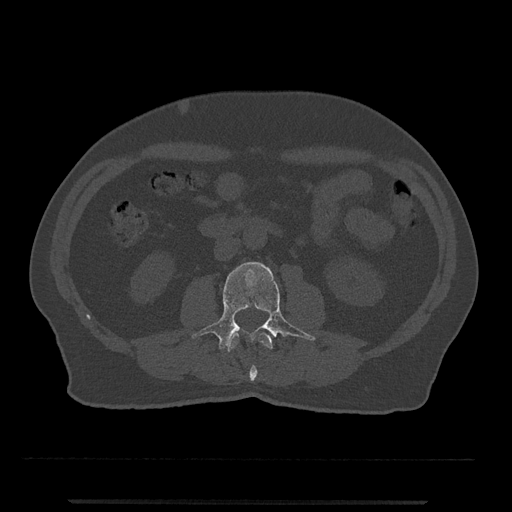
CT including the spine, one axial slice; slice 213 of 797 in the series (ordered by position); reconstruction kernel Br40s/3; 120 kVp; bone window (W 1800 / L 400 HU); 0.5 mm slice thickness; 512 × 512 image matrix, field of view 419 × 419 mm. Male patient, age 63 years. Case-level facts recorded for this patient, not image findings: primary cancer: prostate.
Annotated regions visible in this slice (semi-automatic segmentation, software-assisted and operator-edited):
- L2 vertebra: box from (x=227, y=333) to (x=273, y=381) px
- L3 vertebra: (x=192, y=262)–(x=316, y=350)